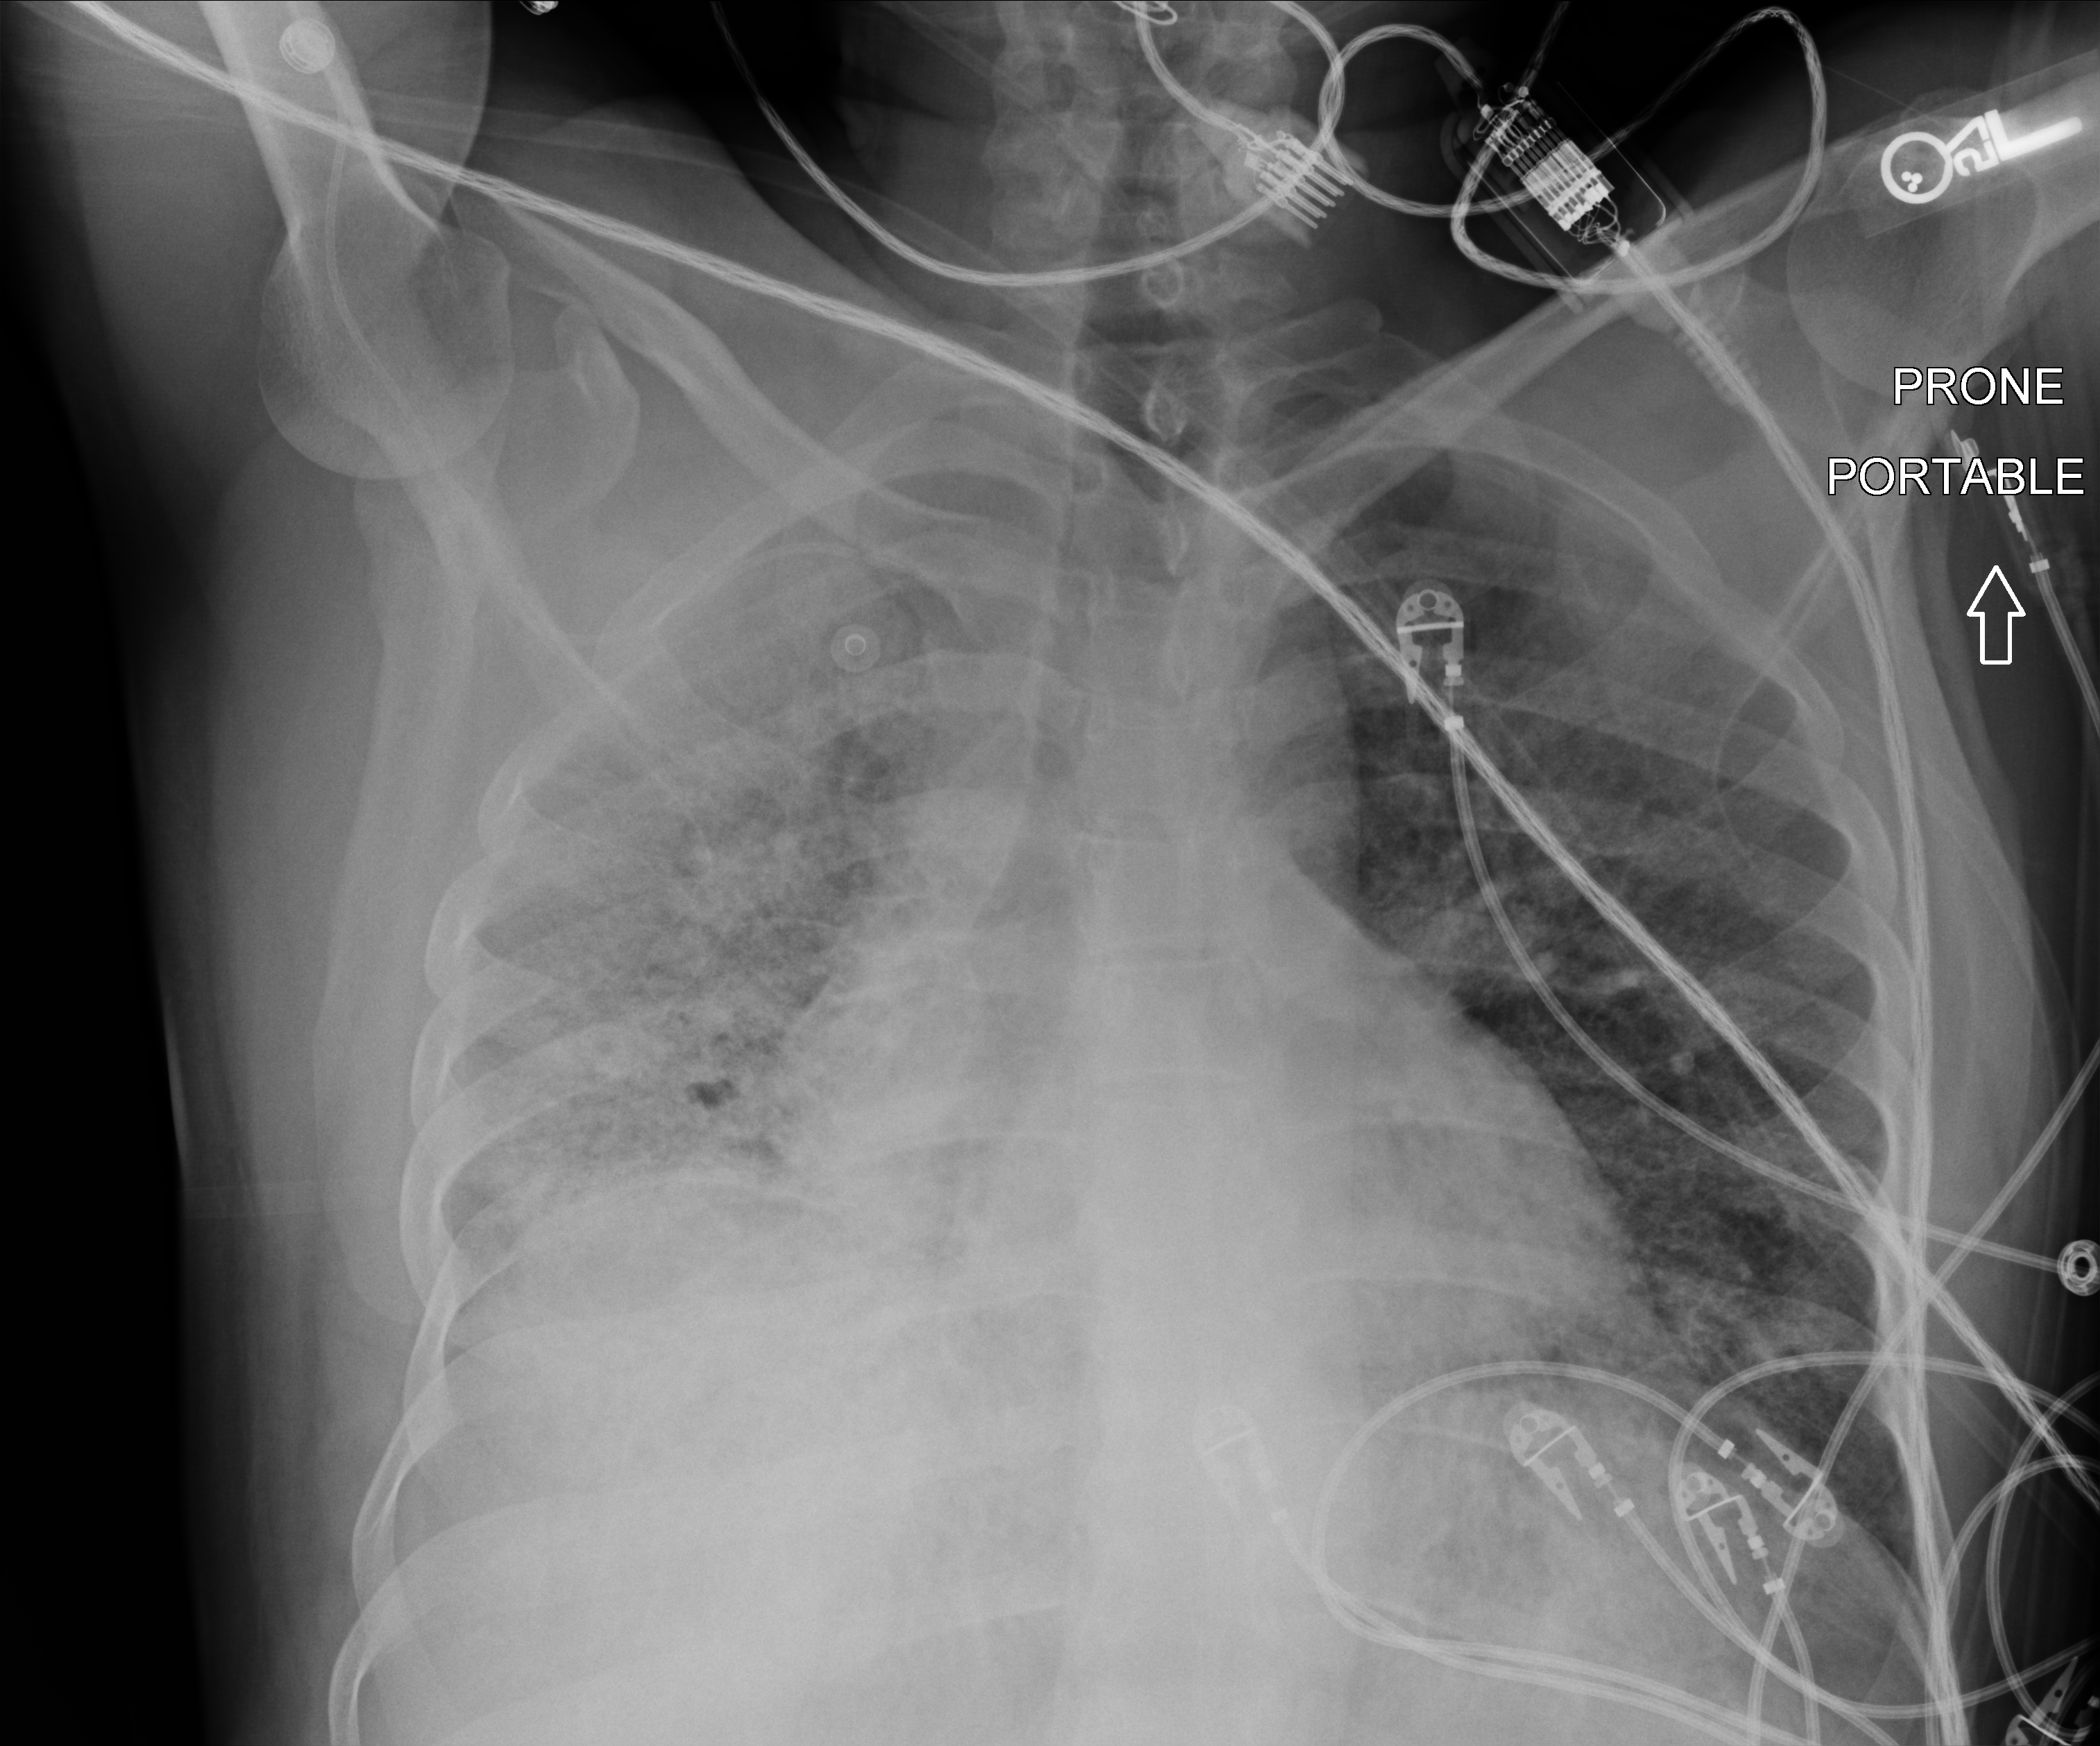
Portable chest radiograph. Adult patient hospitalised with COVID-19, age 18–59 years.
Hospital-stay facts (about this admission, not read from this image; timing relative to this image not recorded): admitted to intensive care during this hospital stay: yes; smoking status (admission record): never.